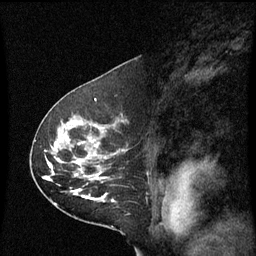
Breast MRI (dynamic contrast-enhanced), one sagittal slice; dynamic contrast-enhanced series, image 2 of 3 at this slice position (ordered by acquisition); 1.5 T; TE 4.2 ms, TR 8.9 ms; 2 mm slice thickness; 256 × 256 image matrix, field of view 200 × 200 mm. Patient: female, 53 years. From the clinical record (not read from this slice): setting: breast cancer imaged before/during neoadjuvant chemotherapy; receptor status: HR-positive, HER2-negative.
Annotated regions visible in this slice (semi-automatic segmentation, software-assisted and operator-edited):
- analysis volume of interest (the breast-tissue region the enhancement analysis was run in; not a lesion): bounding box (x1, y1, x2, y2) in pixels: (32, 100, 129, 221)
- tumour enhancement mask (voxels above the 70 % enhancement threshold inside the analysis volume of interest): (50, 160, 97, 199)